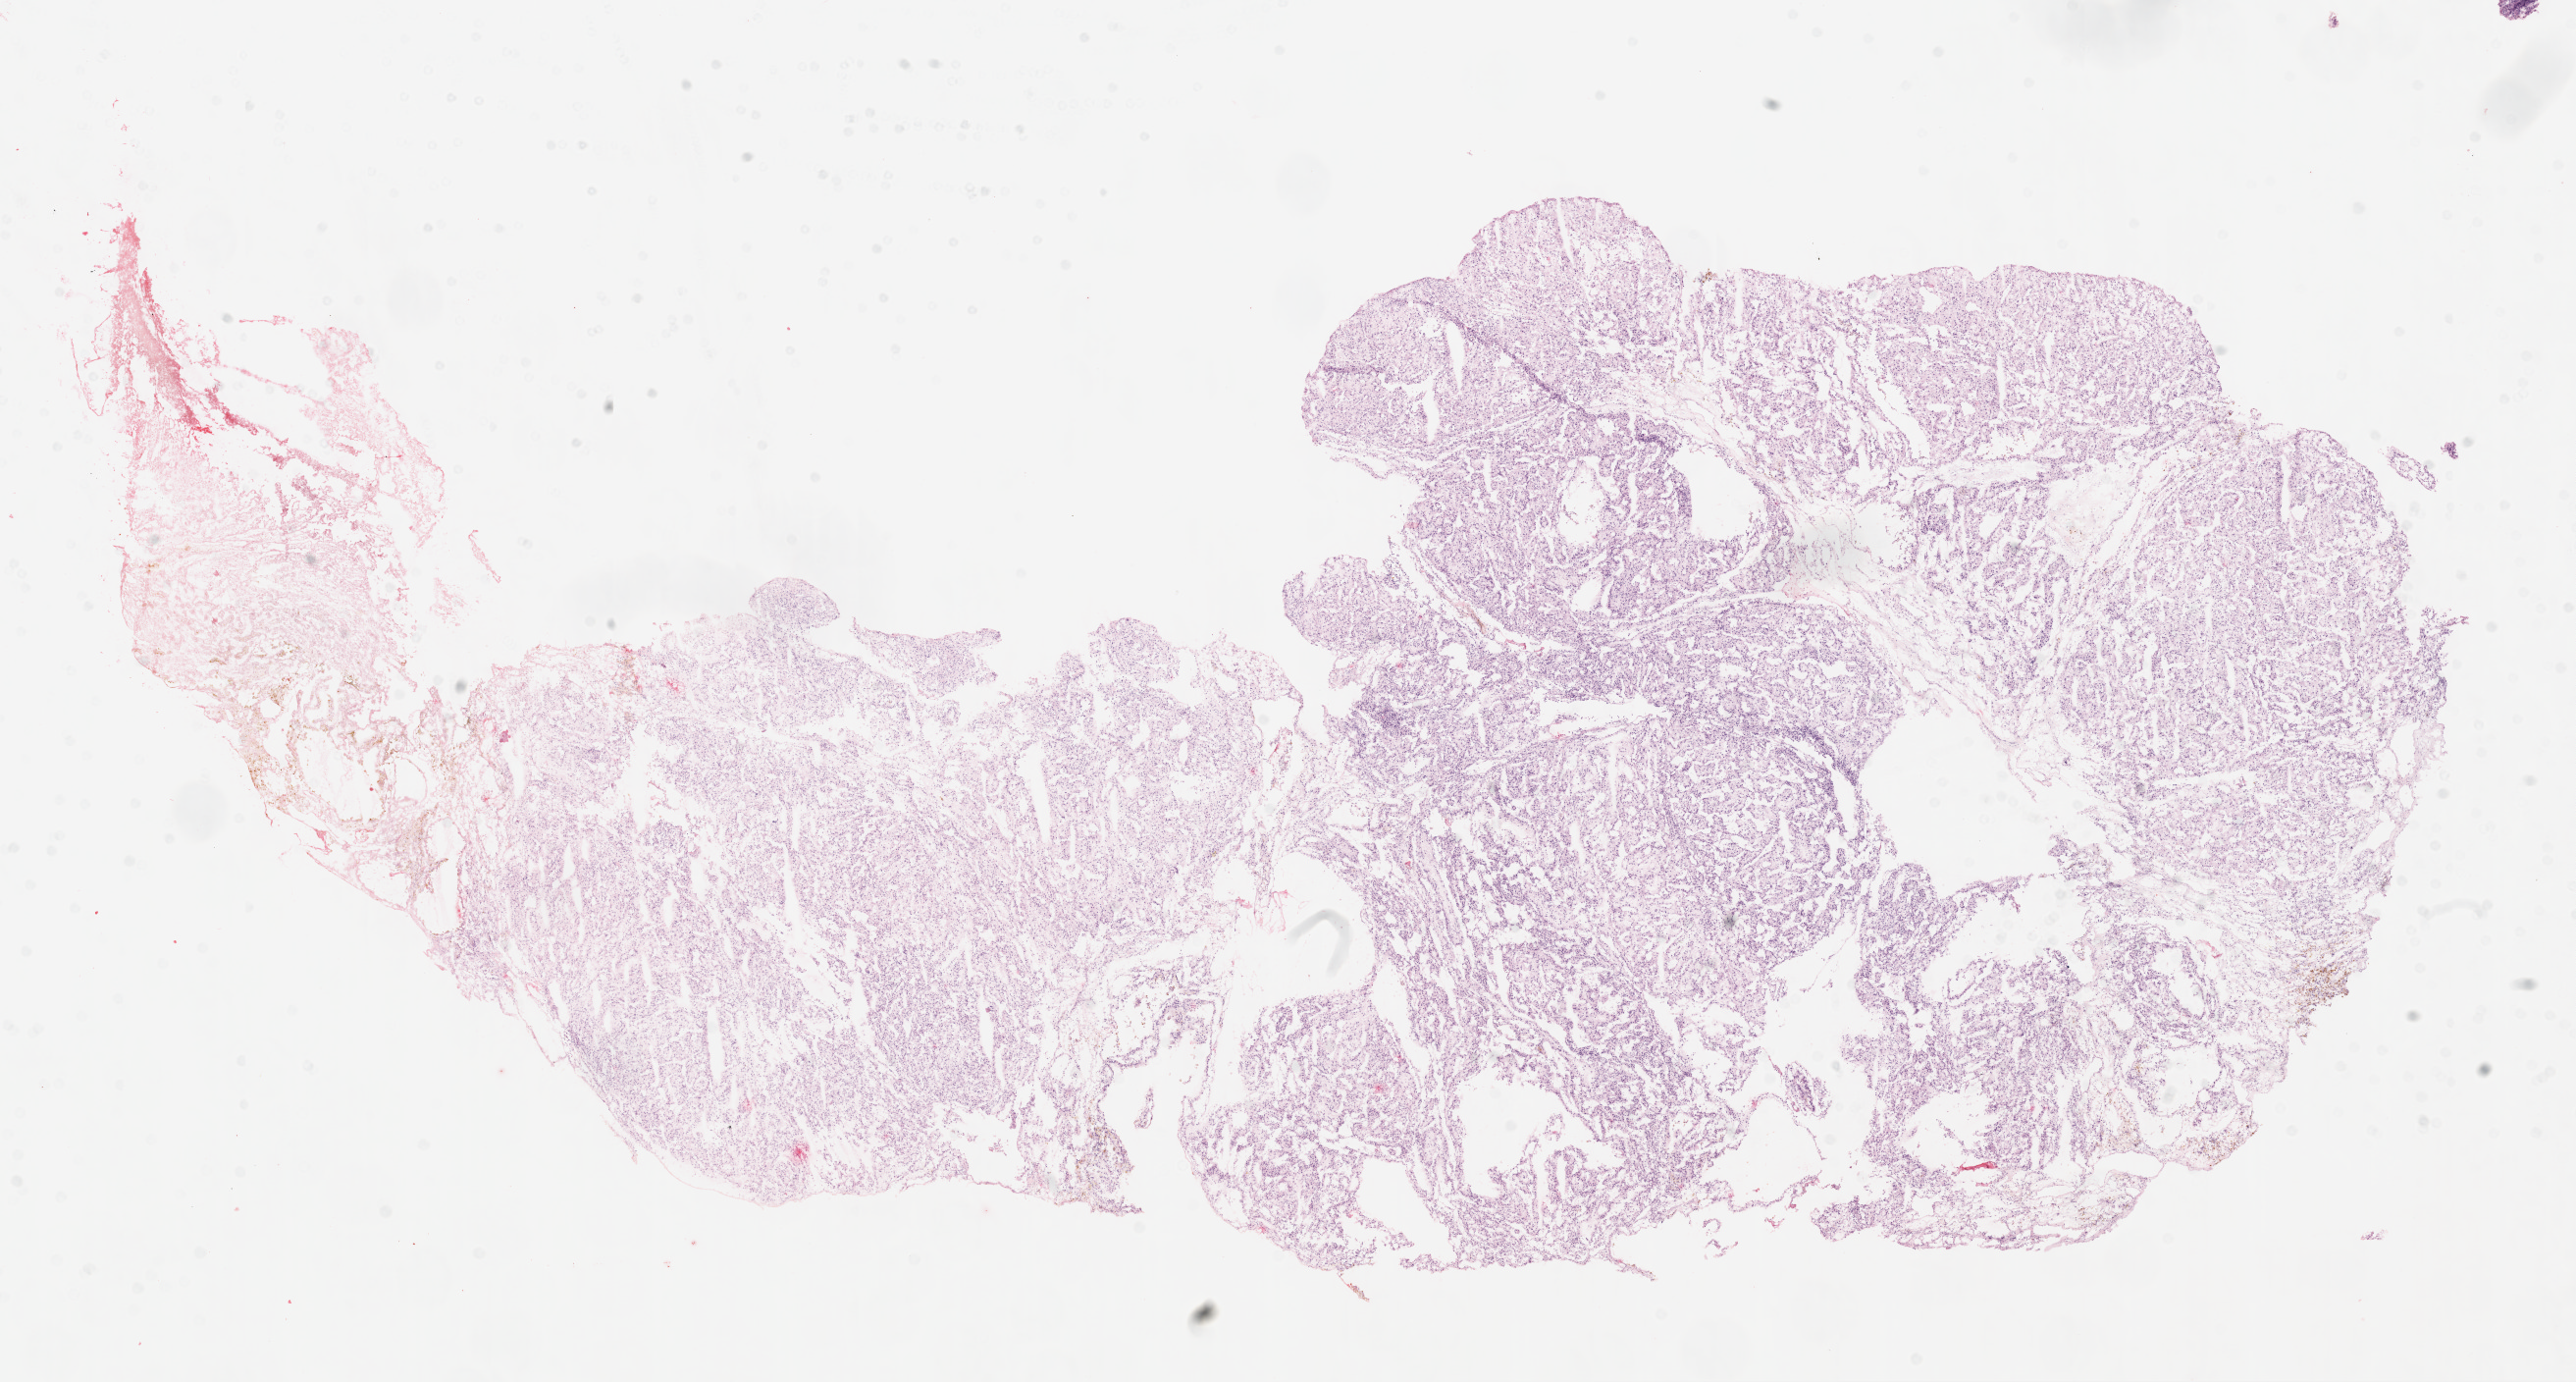
H&E whole-slide image — whole scanned area (about 21.1 x 11.3 mm, from a 20x scan) shown as a low-resolution overview, frozen section from the top of the tissue portion, sample: primary tumour, kidney. Female, age 79 years at initial diagnosis. Histologic grade: G3 (poorly differentiated). Composition of this section per pathologist review: tumour cells 90%, tumour nuclei 85%, normal cells 0%, stromal cells 10%, necrosis 0%.
- laterality: right
- AJCC pathologic stage: I
- pathologic diagnosis: Clear cell adenocarcinoma, NOS